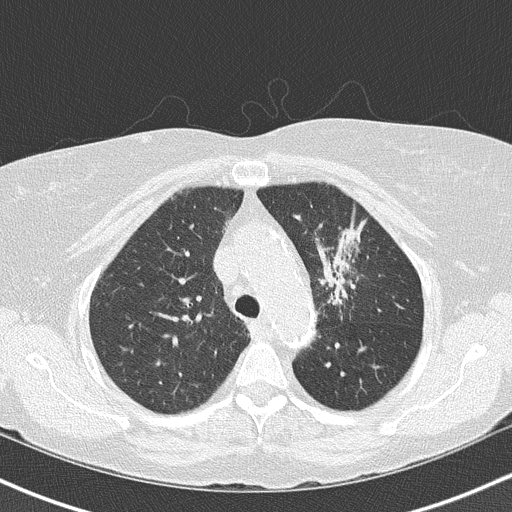
Low-dose screening chest CT, axial slice. Third annual screen. Lung window (W 1500 / L -600 HU). 512 × 512 image matrix. Female participant, aged 68 years at enrolment.
Expert reader's lesion annotation, bounding box [x1, y1, x2, y2] px = [302, 208, 383, 317]. The exam's reader record, not a measurement of the box and not confirmed to be the same lesion: non-calcified nodule or mass ≥4 mm, left upper lobe, 5 × 5 mm, poorly defined margins, mixed attenuation, pre-existing on the prior screen: yes; interval growth: yes. Participant outcome: lung cancer diagnosed 42 days after this screen — adenocarcinoma, NOS, left upper lobe, poorly differentiated (G3), stage IB (AJCC 6th edition), 50 mm at pathology.